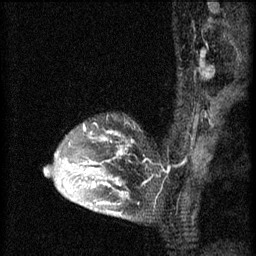
Breast MRI (dynamic contrast-enhanced), one sagittal slice. Position 46 of 60 along the scan axis. 3 images stored at this slice position (order not interpretable as contrast timing). 1.5 T. TE 4.2 ms, TR 8.2 ms. 2 mm slice thickness. 256 × 256 image matrix, field of view 180 × 180 mm. Female patient, age 45 years.
Annotated regions visible in this slice (semi-automatically segmented with operator editing):
- analysis volume of interest (the breast-tissue region the enhancement analysis was run in; not a lesion): box from (x=54, y=124) to (x=145, y=217) px
- tumour enhancement mask (voxels above the 70 % enhancement threshold inside the analysis volume of interest): (x=70, y=124)–(x=129, y=215)